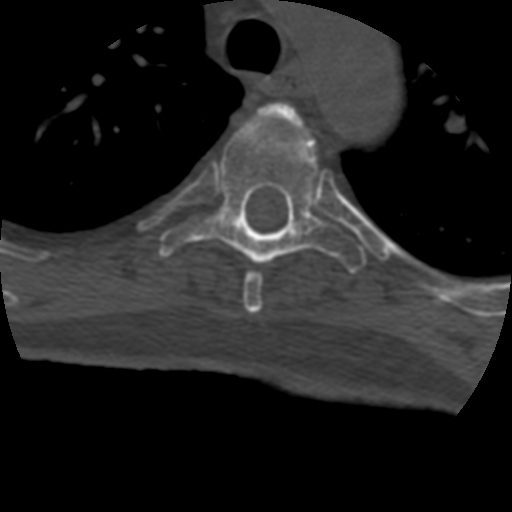
CT including the spine, one axial slice. Slice 322 of 399 in the series (ordered by position). Reconstruction kernel STANDARD. 120 kVp. Bone window (W 1800 / L 400 HU). 512 × 512 image matrix, field of view 160 × 160 mm. Patient age 69 years. Case-level facts recorded for this patient, not image findings: primary cancer: prostate.
Outlined on this slice (semi-automatic segmentation, software-assisted and operator-edited):
- T4 vertebra: bounding box <243,102,304,313> (left, top, right, bottom; pixels)
- T5 vertebra: <160,111,367,272>